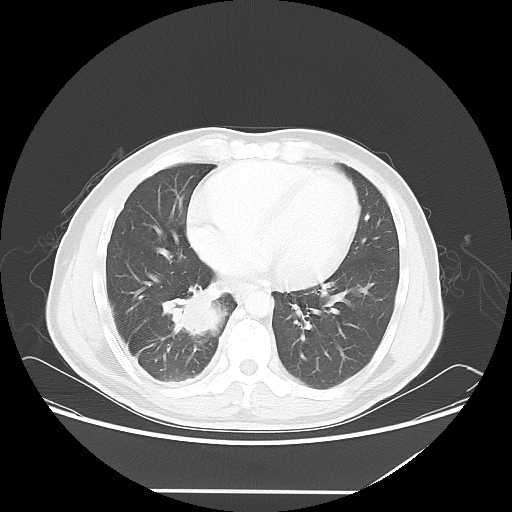
Chest CT, one axial slice. Position 24 of 60 along the scan axis. Lung window (W 1500 / L -600 HU). 512 × 512 image matrix. Patient: male, 48 years. Case-level facts recorded for this patient, not image findings: clinical TNM (as recorded): T3 N3 M1a.
Outlined on this slice (rectangle marked by the reading radiologist):
- lung tumour (recorded histology: squamous cell carcinoma): bounding box <159,284,231,341> (left, top, right, bottom; pixels)